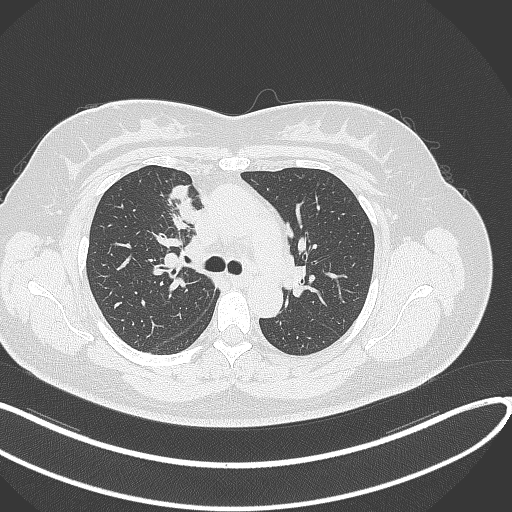
Chest CT, one axial slice; reconstruction kernel B70f; lung window (W 1500 / L -600 HU); 512 × 512 image matrix. Female patient, age 46 years. From the clinical record (not read from this slice): clinical TNM (as recorded): T2a N1 M0.
Annotated regions visible in this slice (rectangle marked by the reading radiologist):
- lung tumour (recorded histology: adenocarcinoma): bounding box <167,182,202,226> (left, top, right, bottom; pixels)